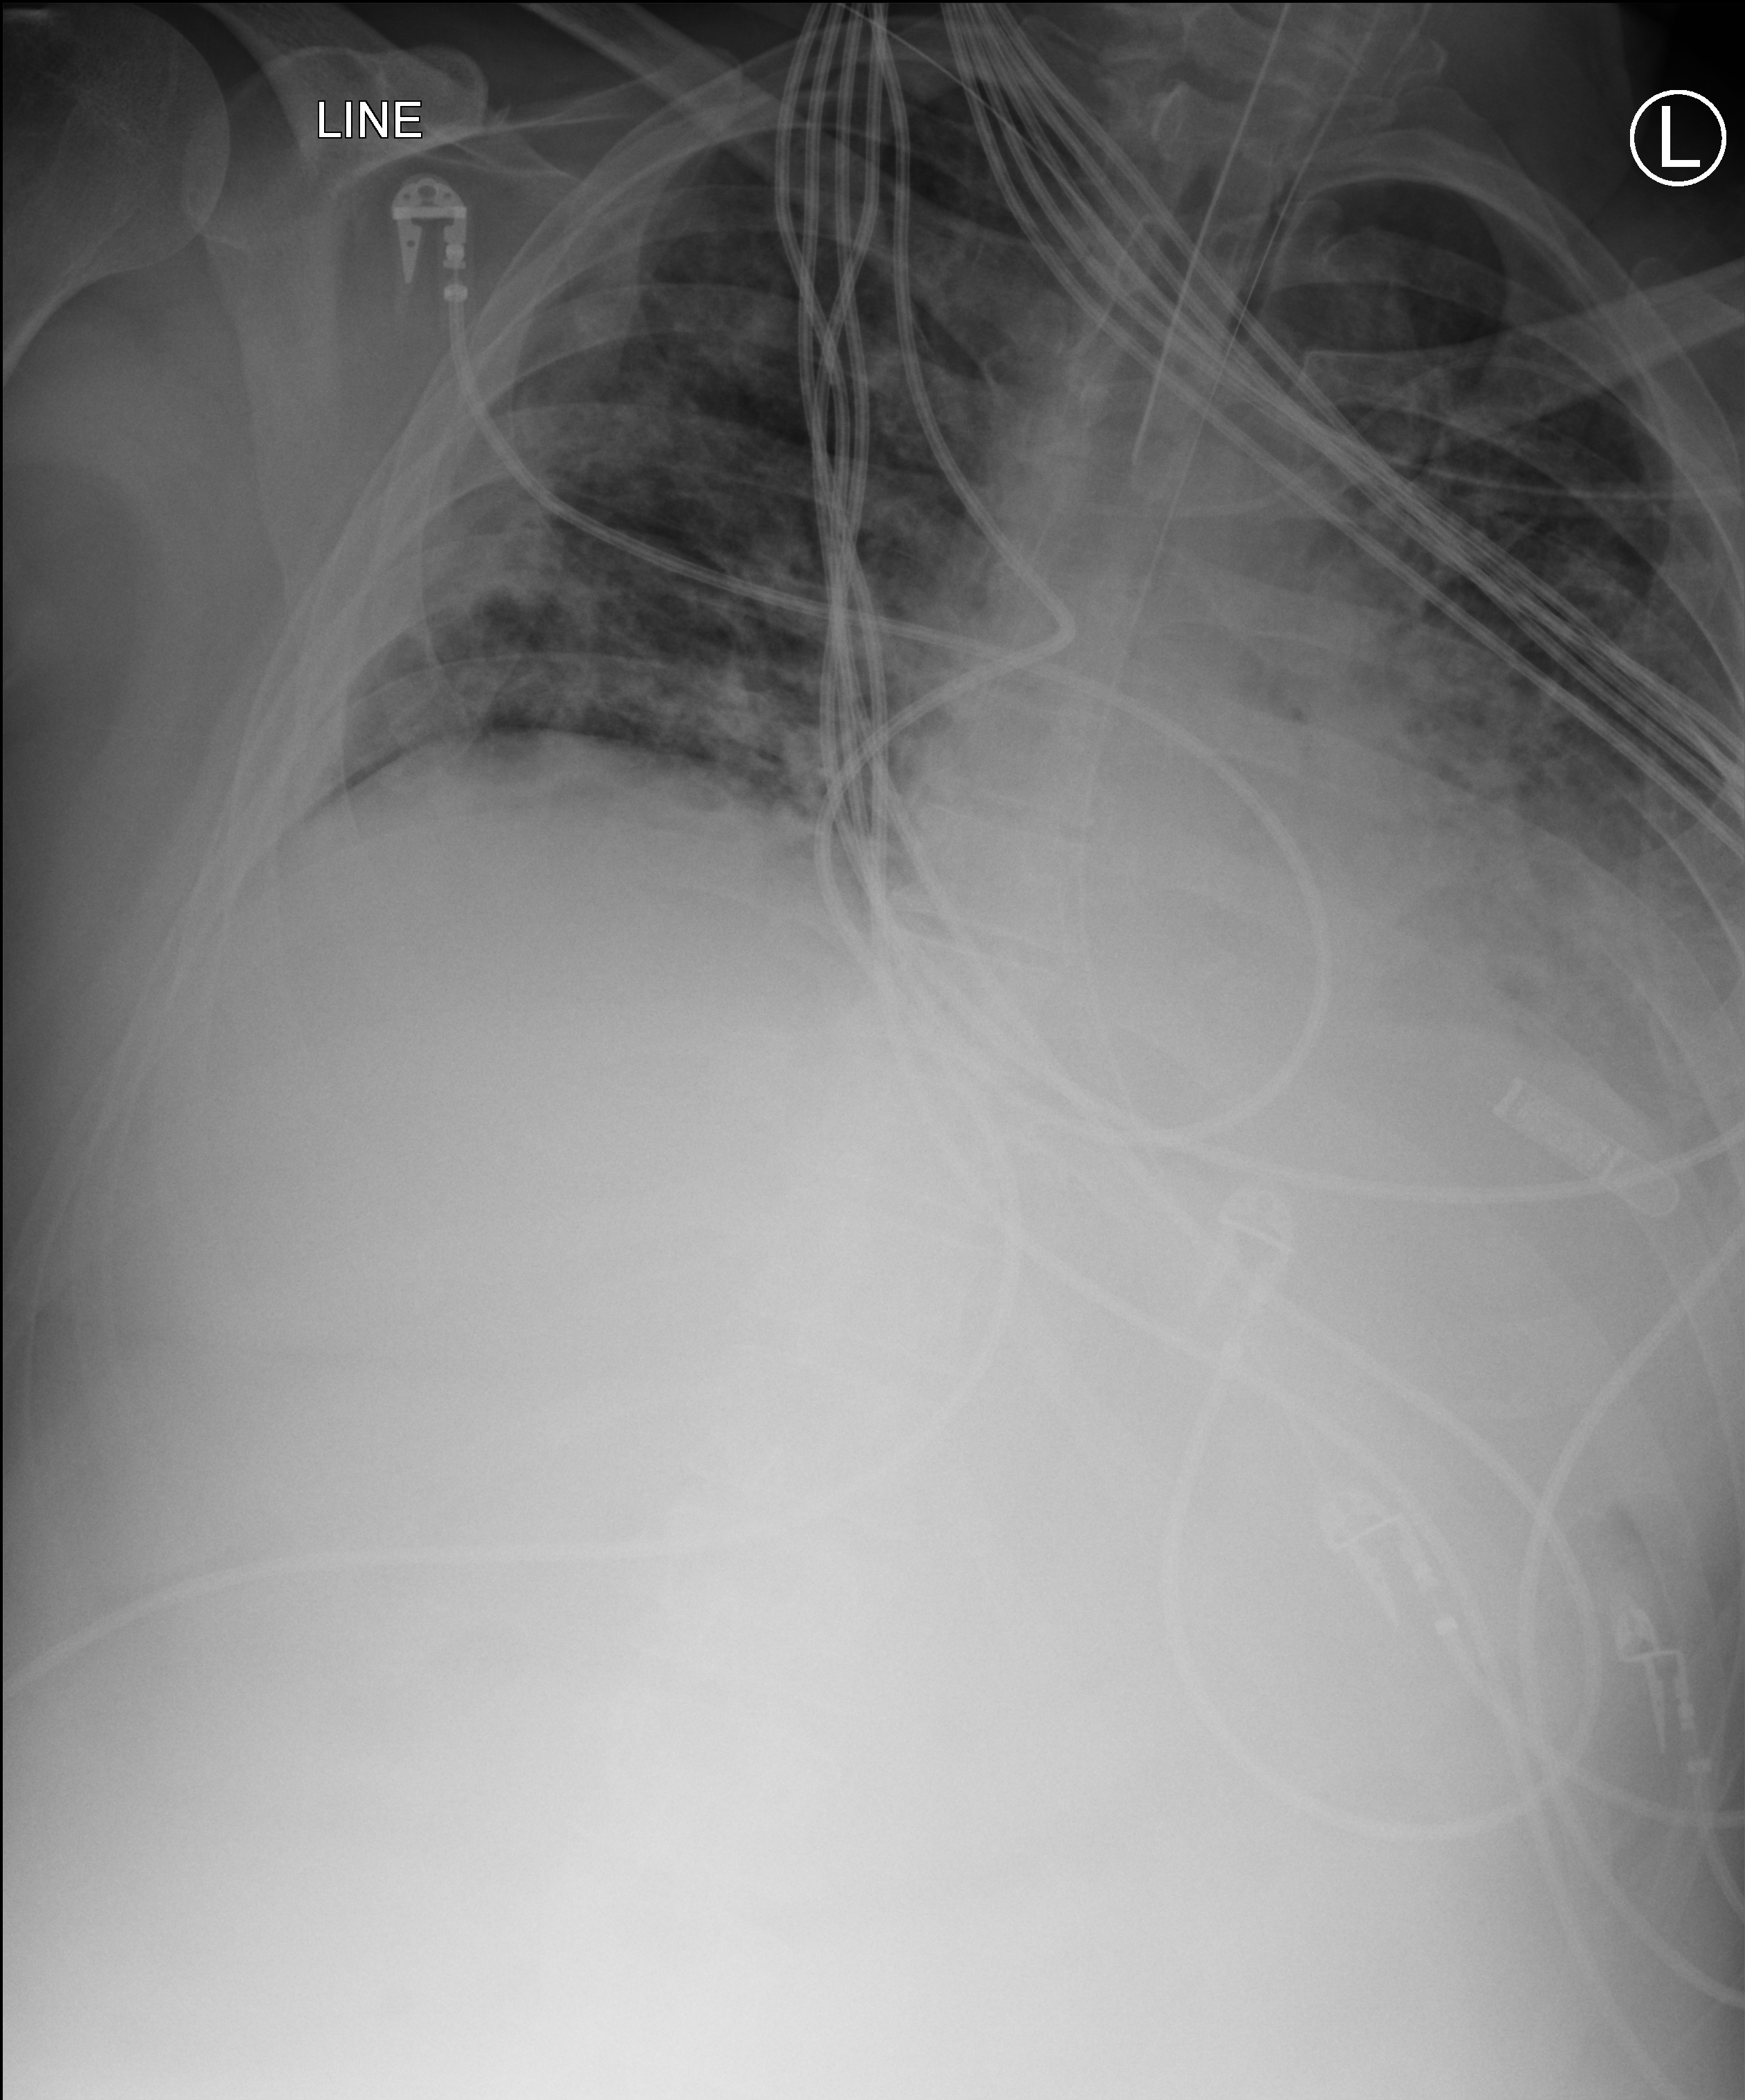
Bedside chest radiograph (computed radiography). Male patient hospitalised with COVID-19, age 18–59 years.
Hospital-stay facts (about this admission, not read from this image; timing relative to this image not recorded): length of hospital stay: 39 days; mechanically ventilated during this hospital stay: yes.